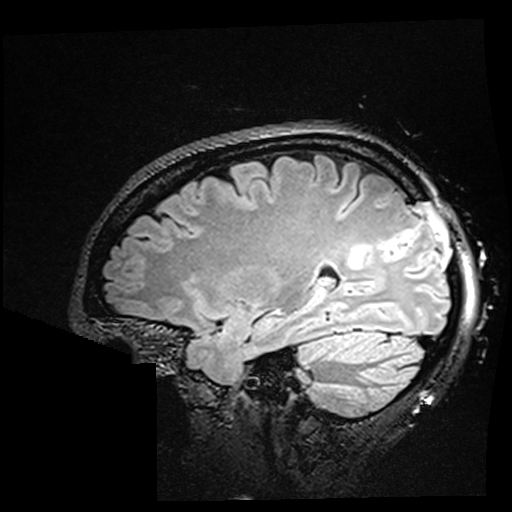
Brain MRI from a brain-tumour surgery series, one sagittal slice; slice 119 of 176 in the series (ordered by position); T2 FLAIR; 512 × 512 image matrix, field of view 250 × 250 mm. Case-level facts recorded for this patient, not image findings: histopathology: Oligodendroglioma; WHO grade: 2; IDH mutation: yes; tumour location: Right Parietal.
Outlined on this slice (outlined manually by an expert reader):
- residual tumour: box from (x=347, y=244) to (x=387, y=274) px